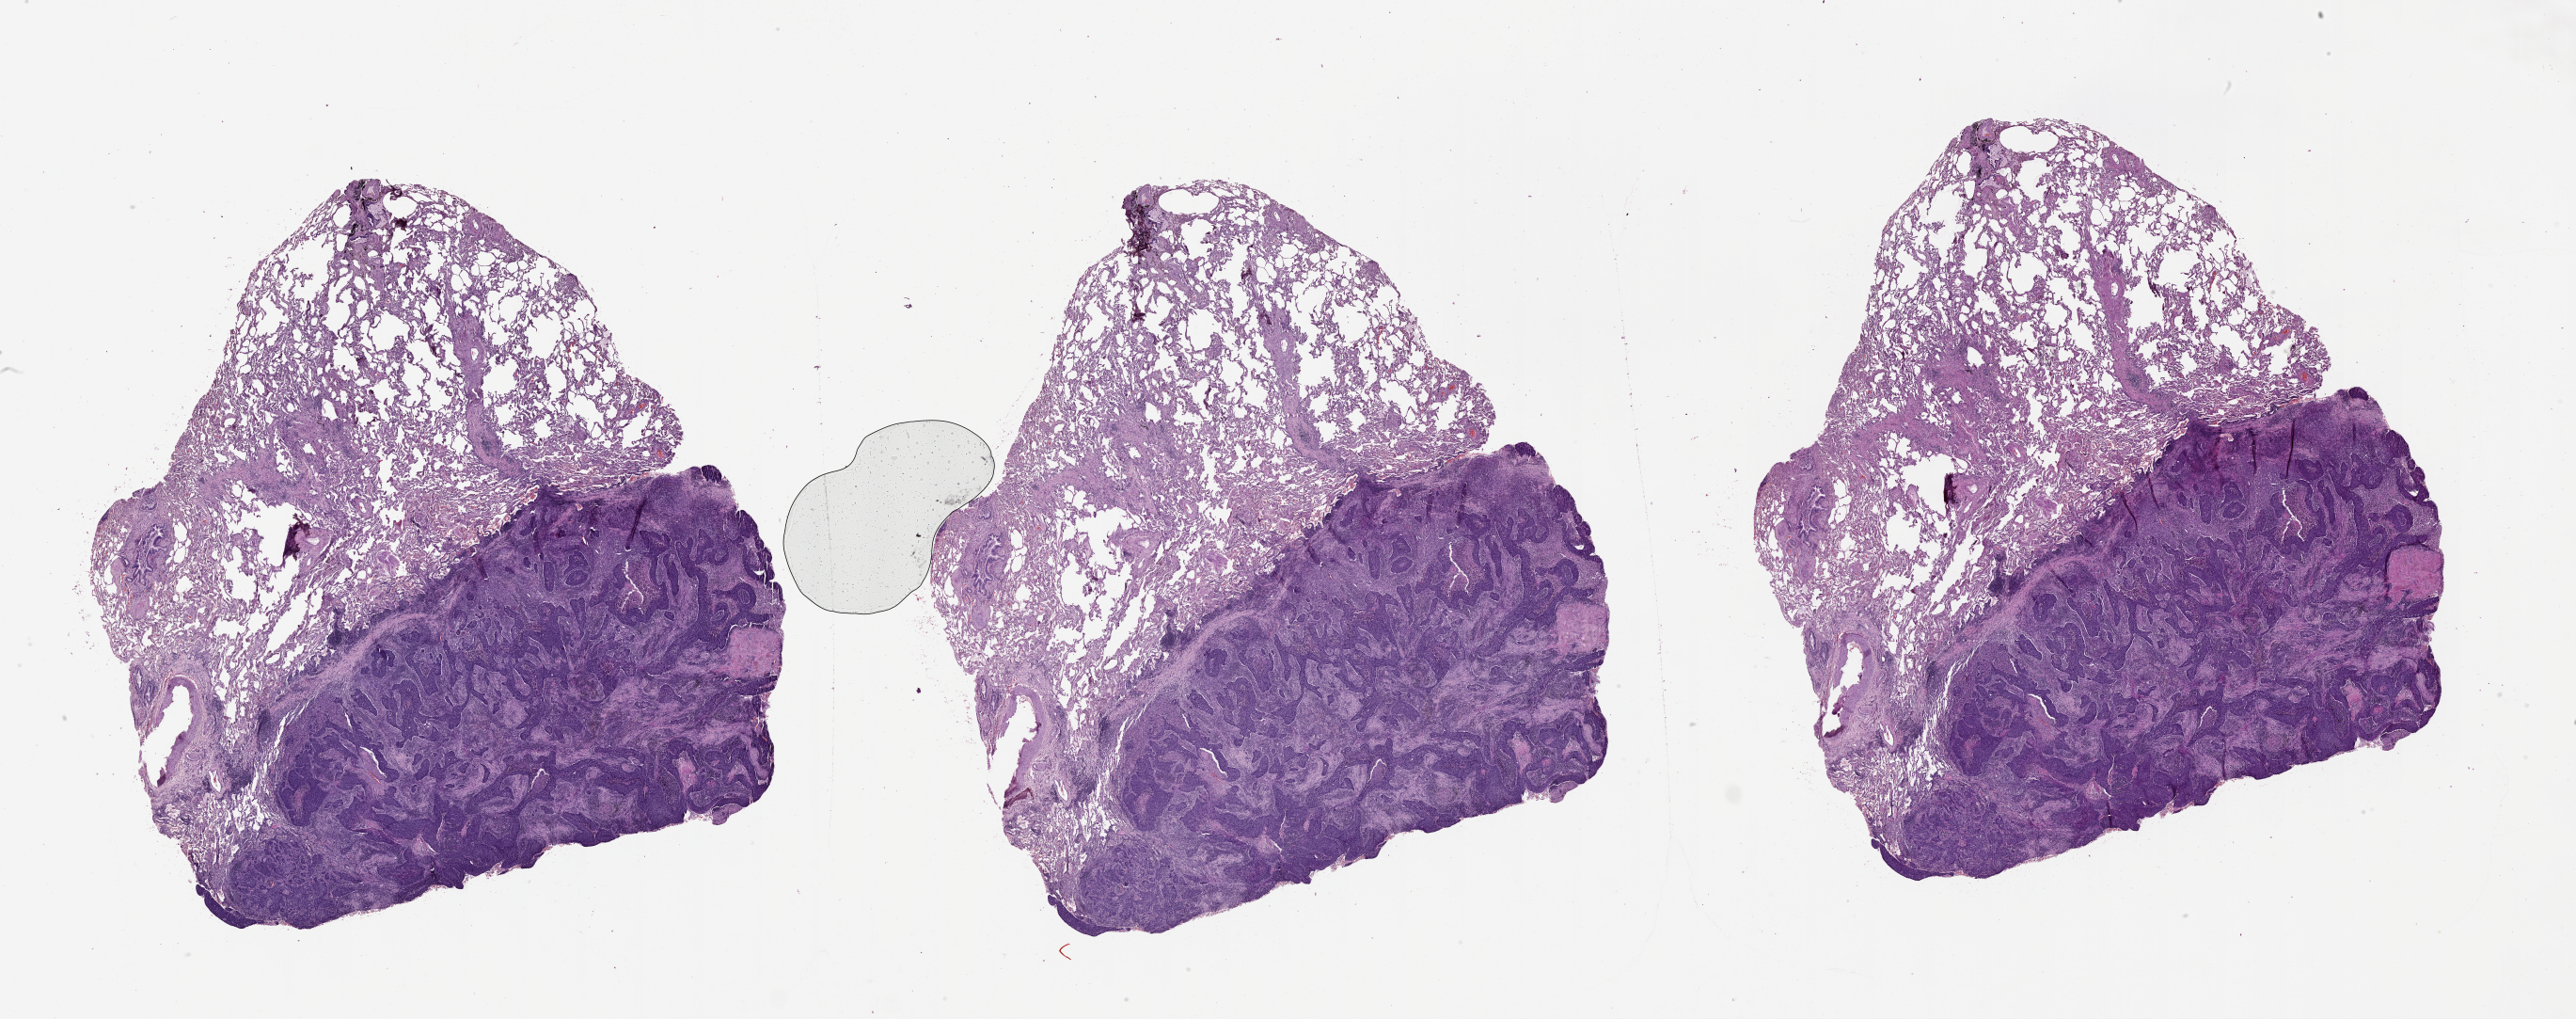
Hematoxylin and eosin (H&E) stained whole-slide image — a low-resolution overview of the entire scanned area, about 44.1 x 17.4 mm; tumour tissue sample, lung. 62-year-old female patient.
Patient diagnosis (cohort enrolment): squamous cell carcinoma (lung).